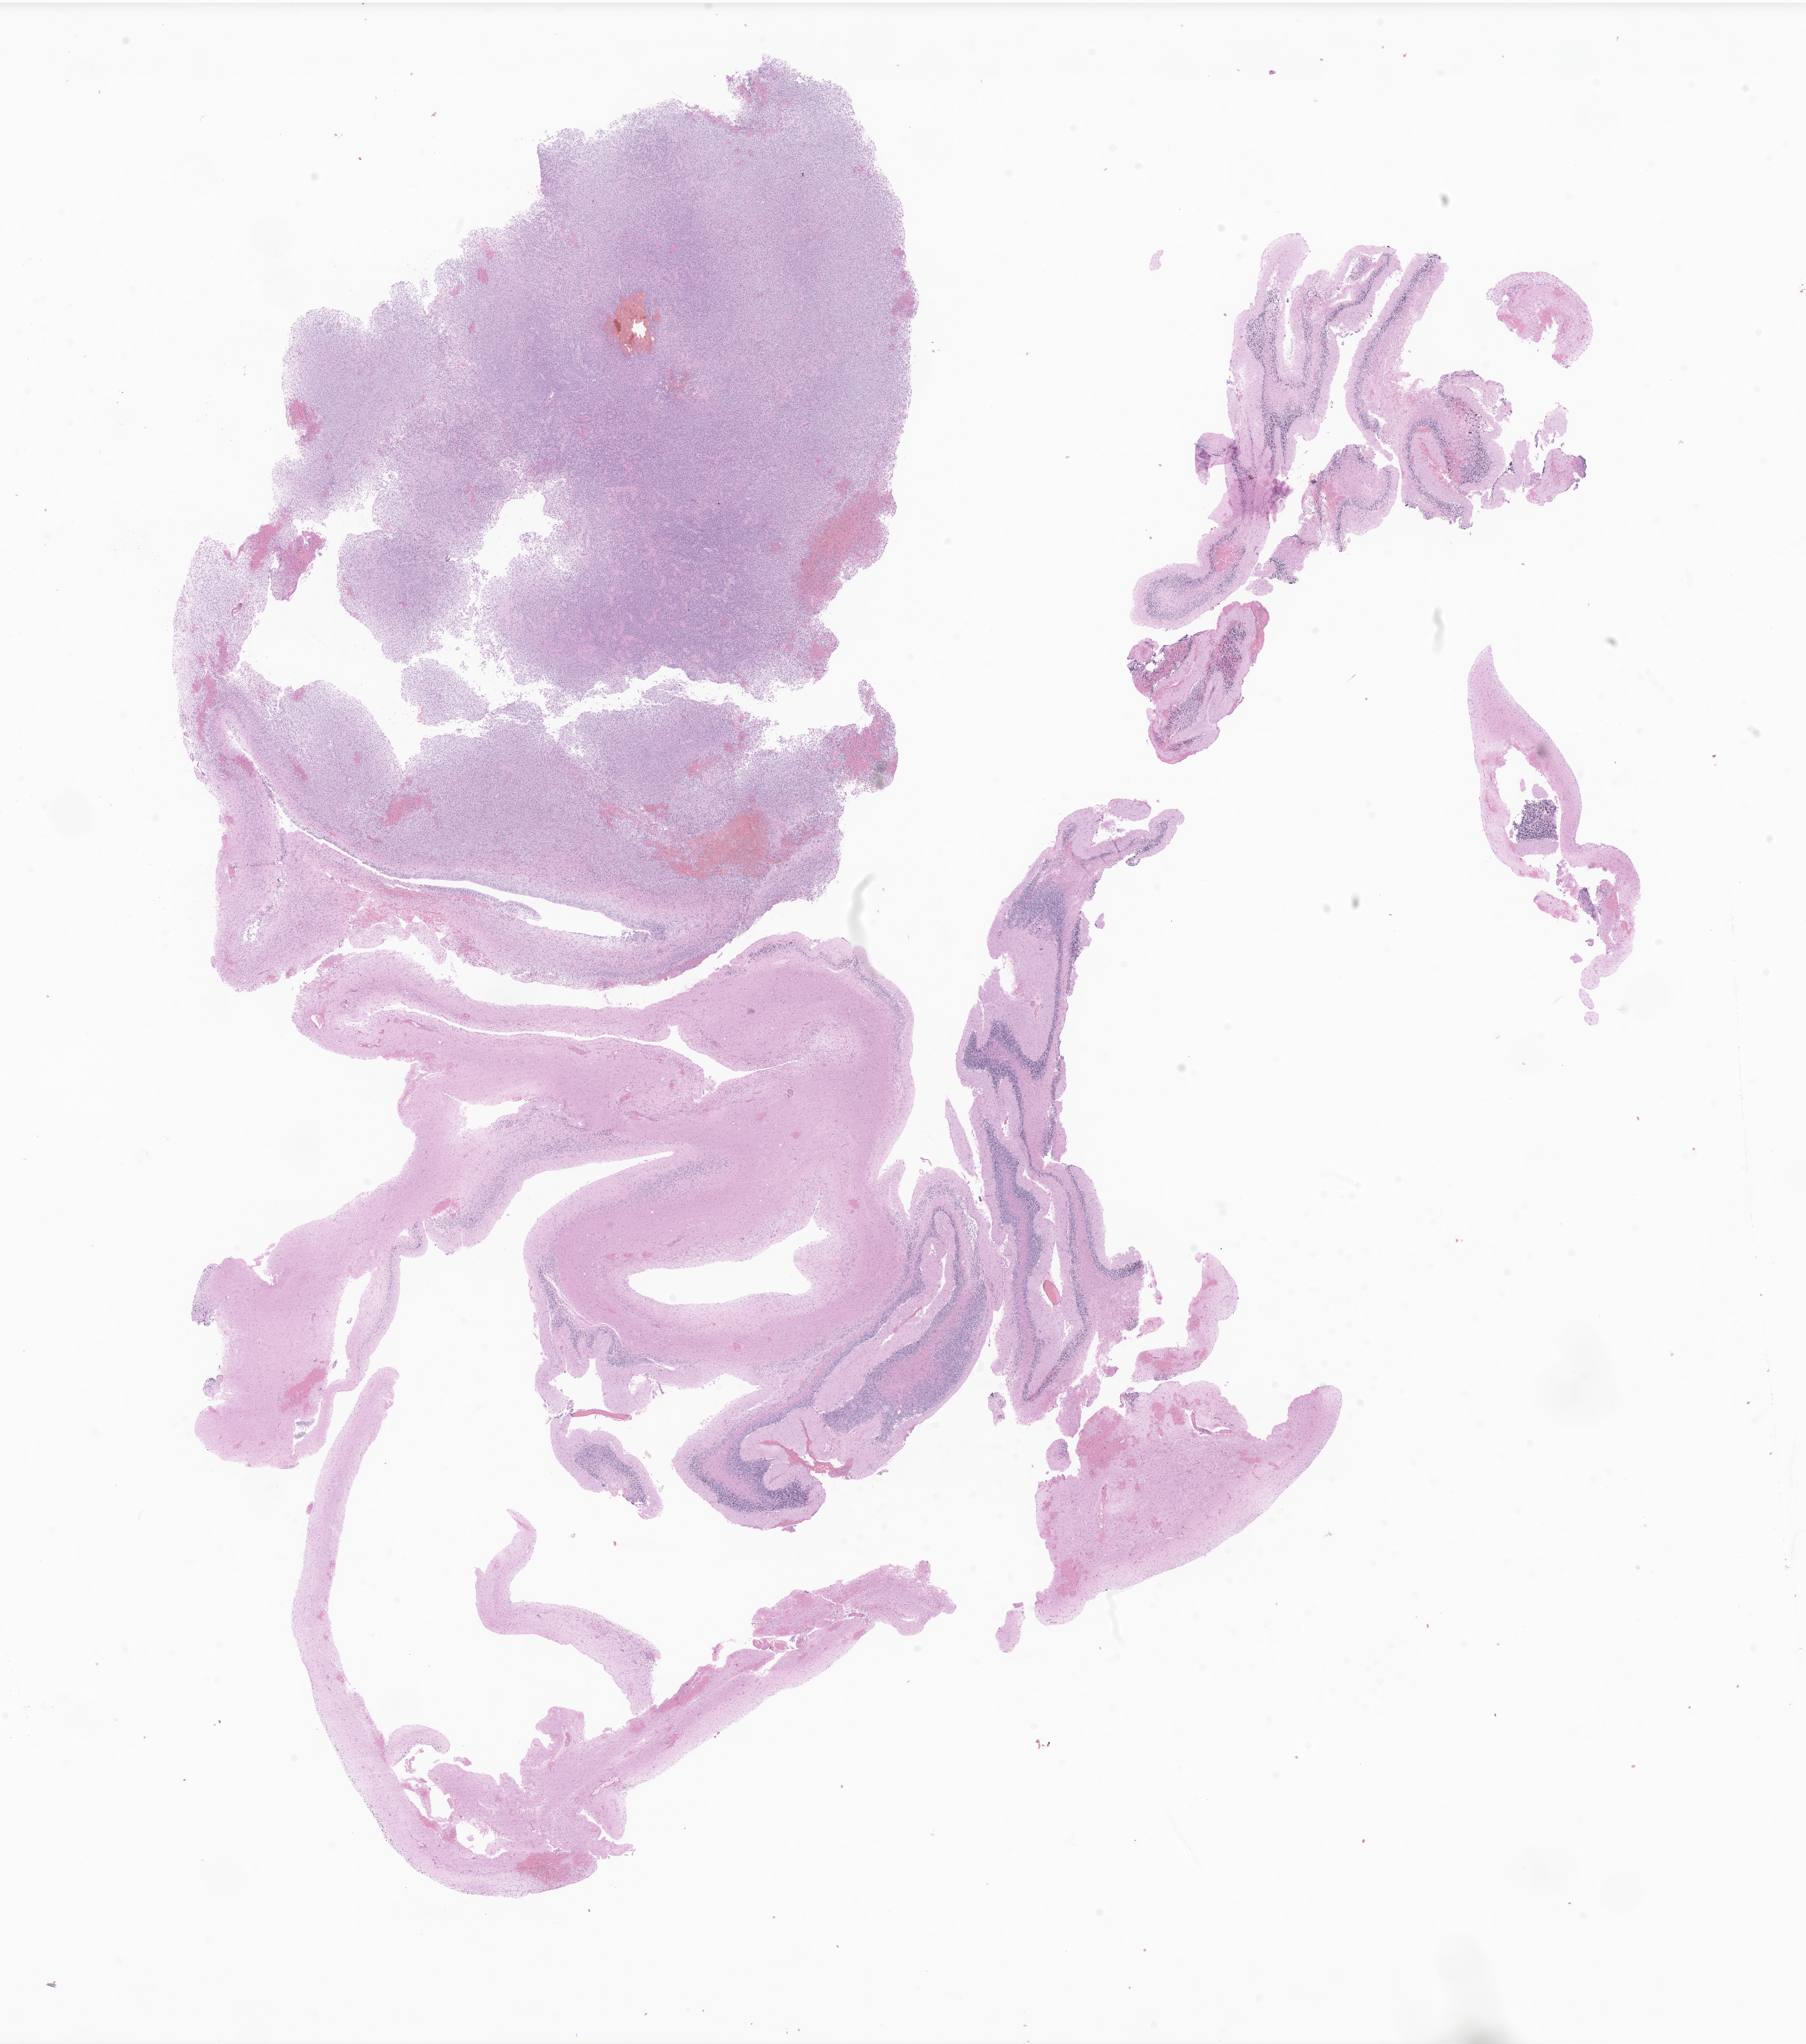
Digitized hematoxylin and eosin (H&E)-stained section of tumor tissue from the brain — whole scanned area (about 20.5 x 23.2 mm) shown as a low-resolution overview. Formalin-fixed, paraffin-embedded (FFPE) tissue. Patient: female, age 196 months (16 years 4 months).
Recorded diagnosis: Pilocytic astrocytoma.